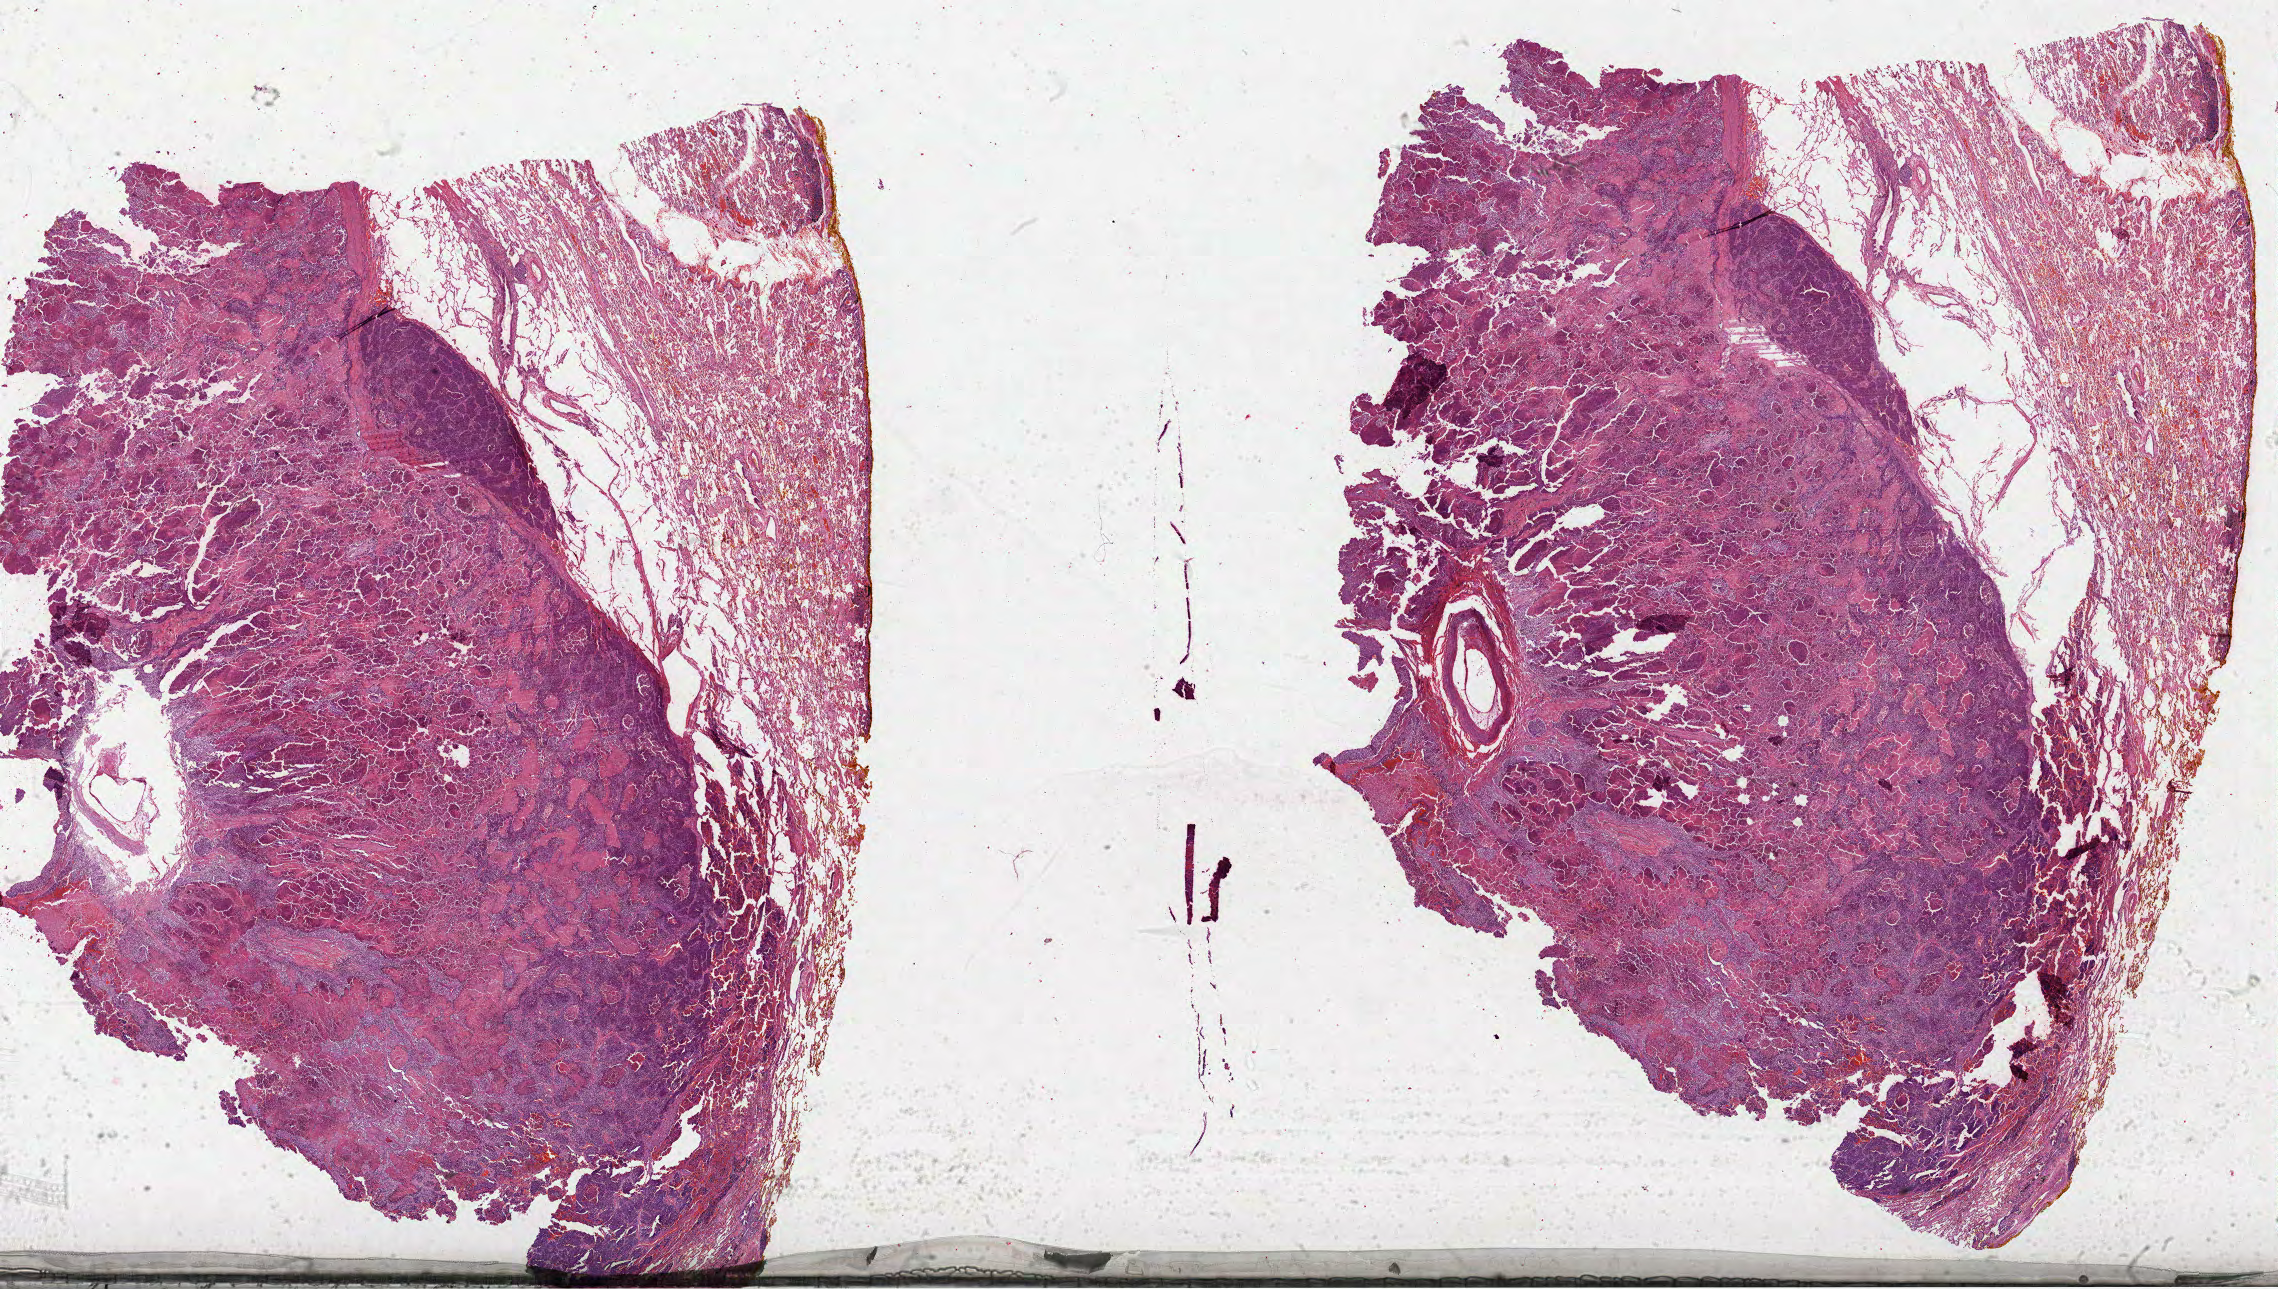
Whole-slide histology image, H&E-stained — shown as a low-resolution overview of the whole scanned area (about 36.7 x 20.8 mm, acquisition: 40x scan). FFPE section. Sample: primary tumour, lung. Male, age 74 years at initial diagnosis.
Histologic diagnosis: Basaloid squamous cell carcinoma (upper lobe, lung). Laterality: right. AJCC pathologic stage: IB (6th edition). TNM: T2 N0 M0.